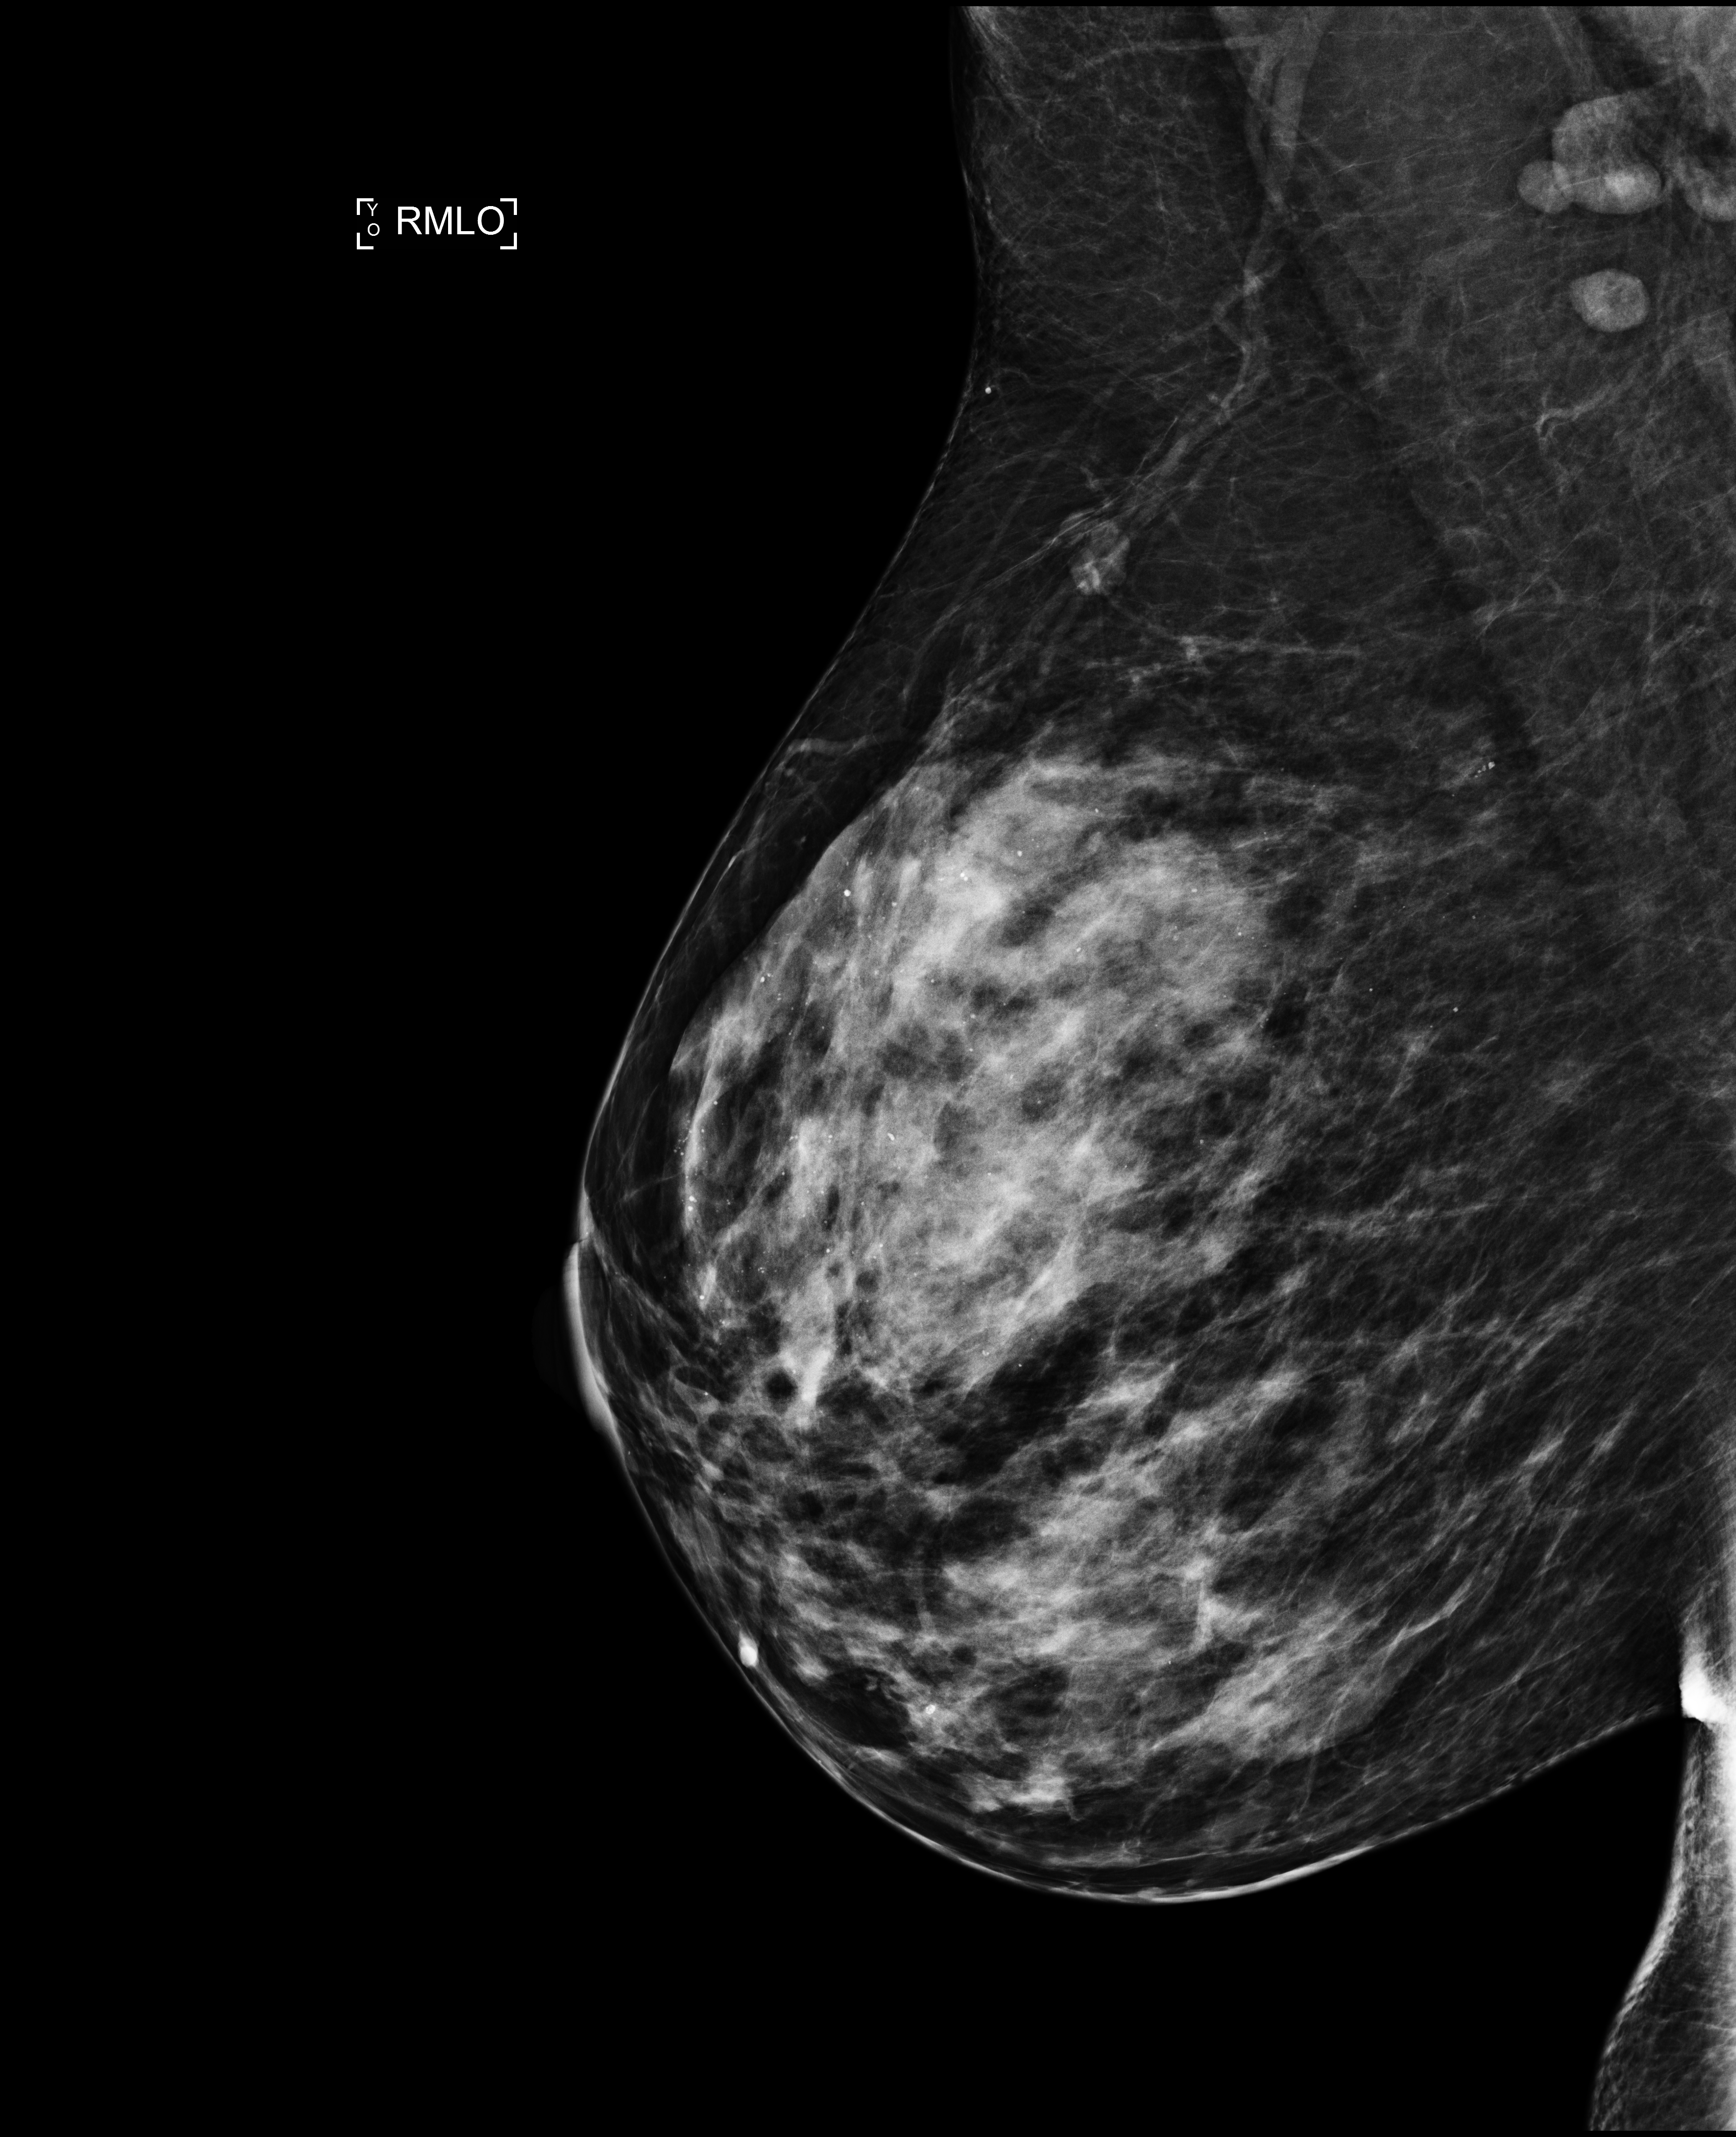
Screening examination, system: Selenia Dimensions. Patient: female, 45 years.
Image type: full-field digital mammogram. Breast: right. Projection: medio-lateral oblique projection.